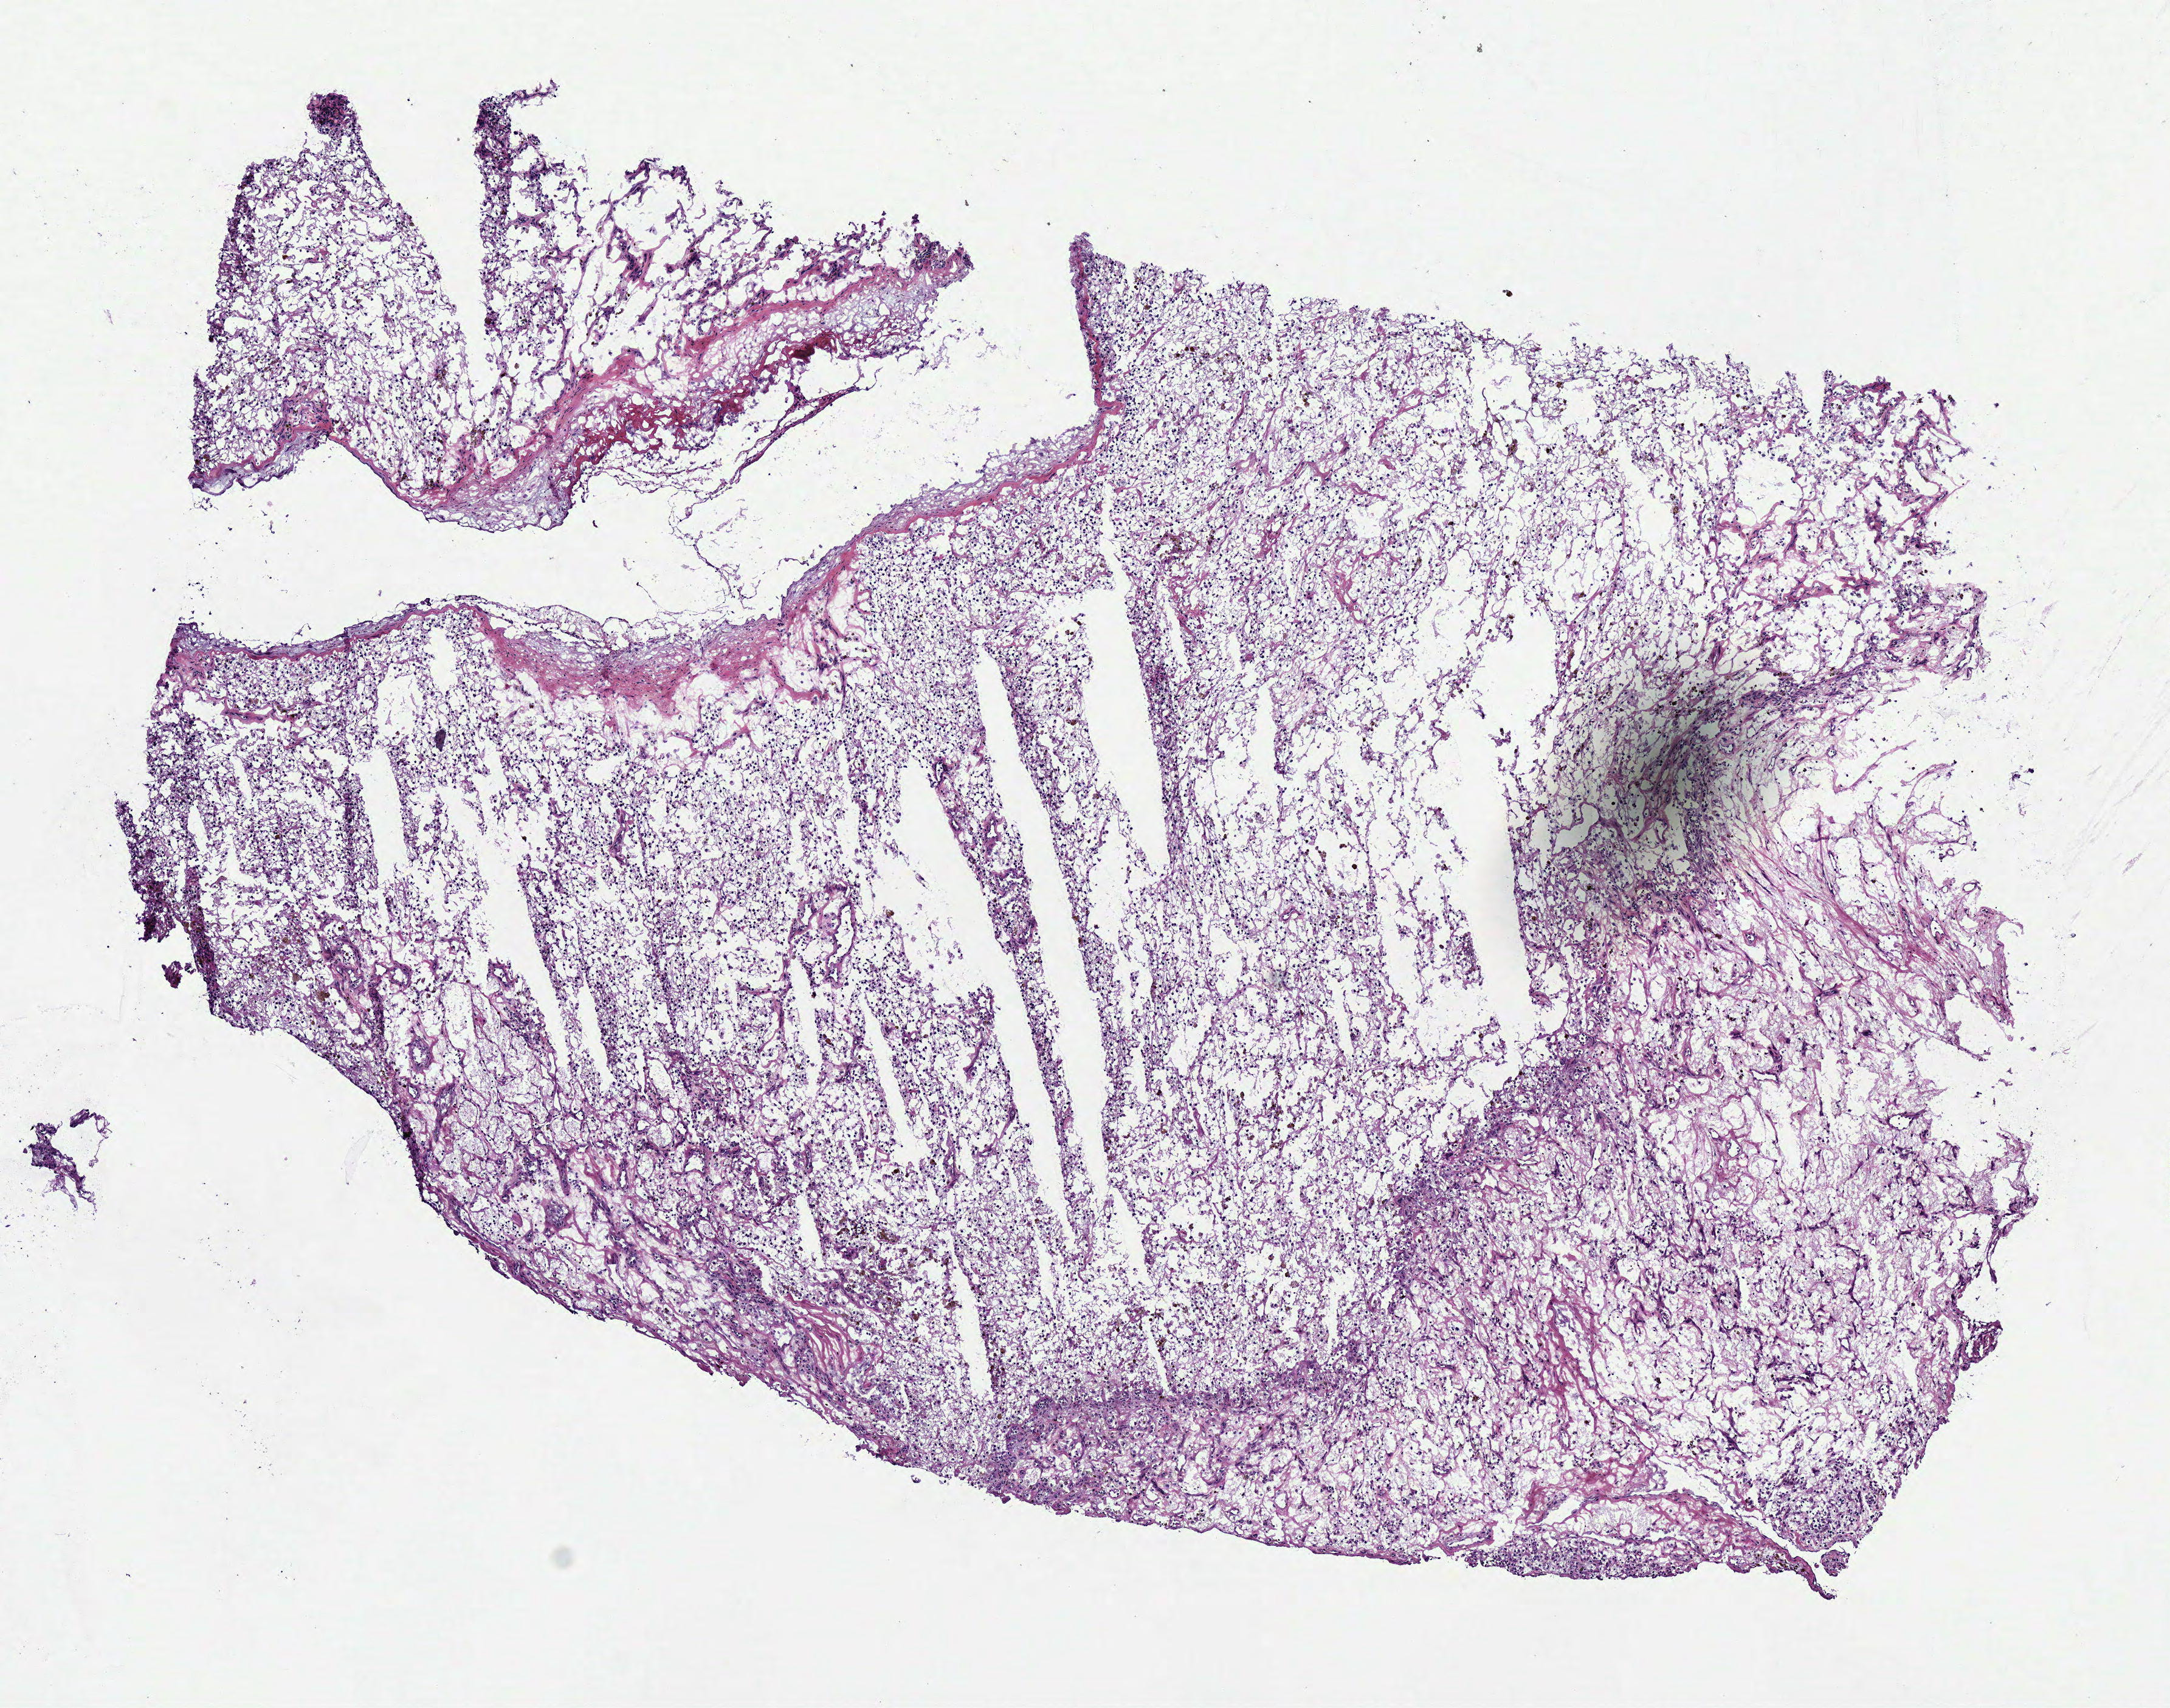
Digitized Hematoxylin and eosin (H&E) stained tissue section (whole slide) — shown as a low-resolution overview of the whole scanned area (about 7.0 x 5.5 mm, from a 40x scan). Frozen section. Kidney, primary tumour sample. Male, age 68 years at initial diagnosis. Histologic grade: G3 (poorly differentiated). Composition of this section per pathologist review: tumour cells 90%, tumour nuclei 85%, normal cells 0%, stromal cells 10%, necrosis 0%.
Laterality: right. AJCC pathologic stage: I. Histologic diagnosis: Clear cell adenocarcinoma, NOS.